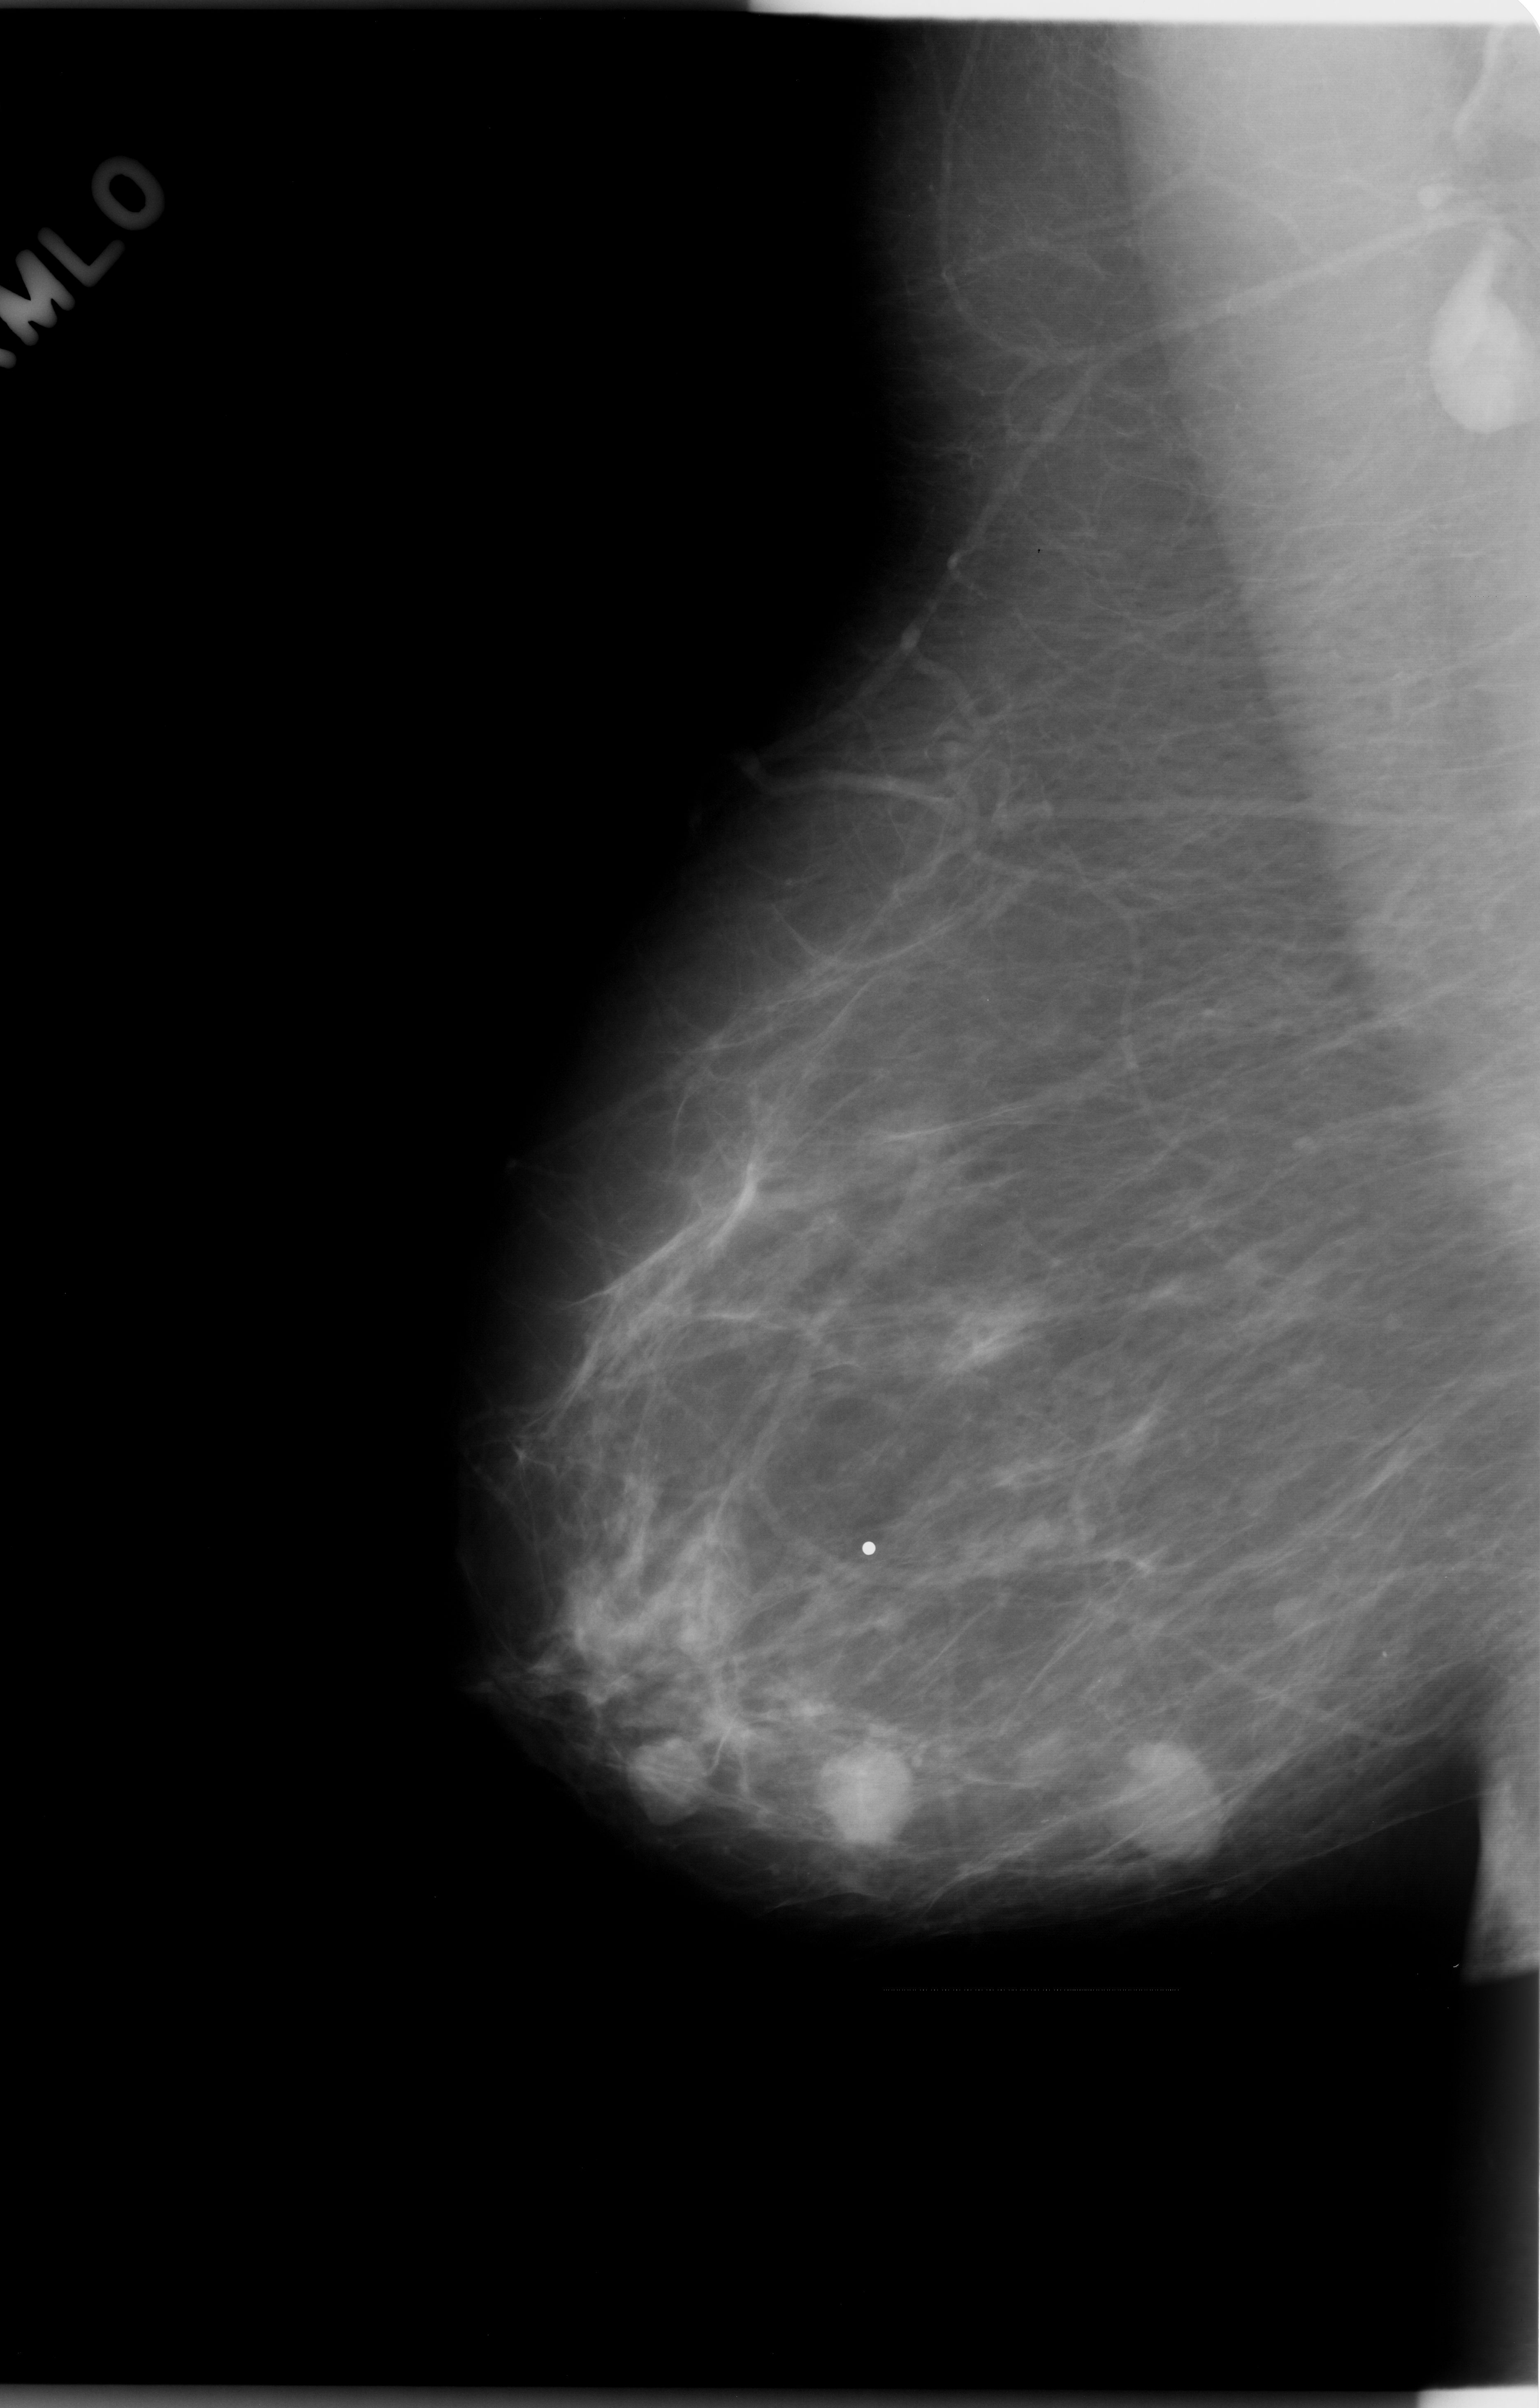
Scanned film-screen mammogram, right breast, MLO view.
Radiologist-marked abnormalities on this image: Finding 1 of 3: mass, shape oval, margins circumscribed; BI-RADS assessment category 4; pathology result (as recorded, not read from the image): benign. Finding 2 of 3: mass, shape oval, margins microlobulated; BI-RADS assessment category 4; pathology (as recorded): malignant. Finding 3 of 3: mass, shape oval, margins microlobulated; BI-RADS assessment category 4; subtlety rating 5 on a 1 (subtle) to 5 (obvious) scale; pathology result (as recorded, not read from the image): malignant.